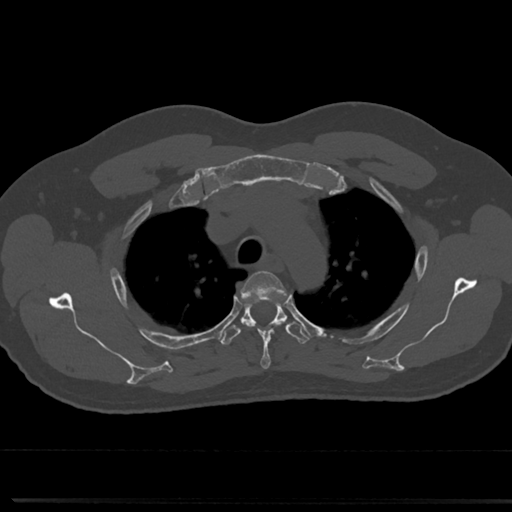
CT including the spine, one axial slice. Position 568 of 817 along the scan axis. Bone window (W 1800 / L 400 HU). 0.5 mm slice thickness. 512 × 512 image matrix, field of view 355 × 355 mm. Patient: male, 61 years. From the clinical record (not read from this slice): primary cancer: prostate.
Annotated regions visible in this slice (semi-automatic segmentation, software-assisted and operator-edited):
- T3 vertebra: bounding box (x1, y1, x2, y2) in pixels: (242, 270, 283, 369)
- T4 vertebra: (219, 299, 310, 346)